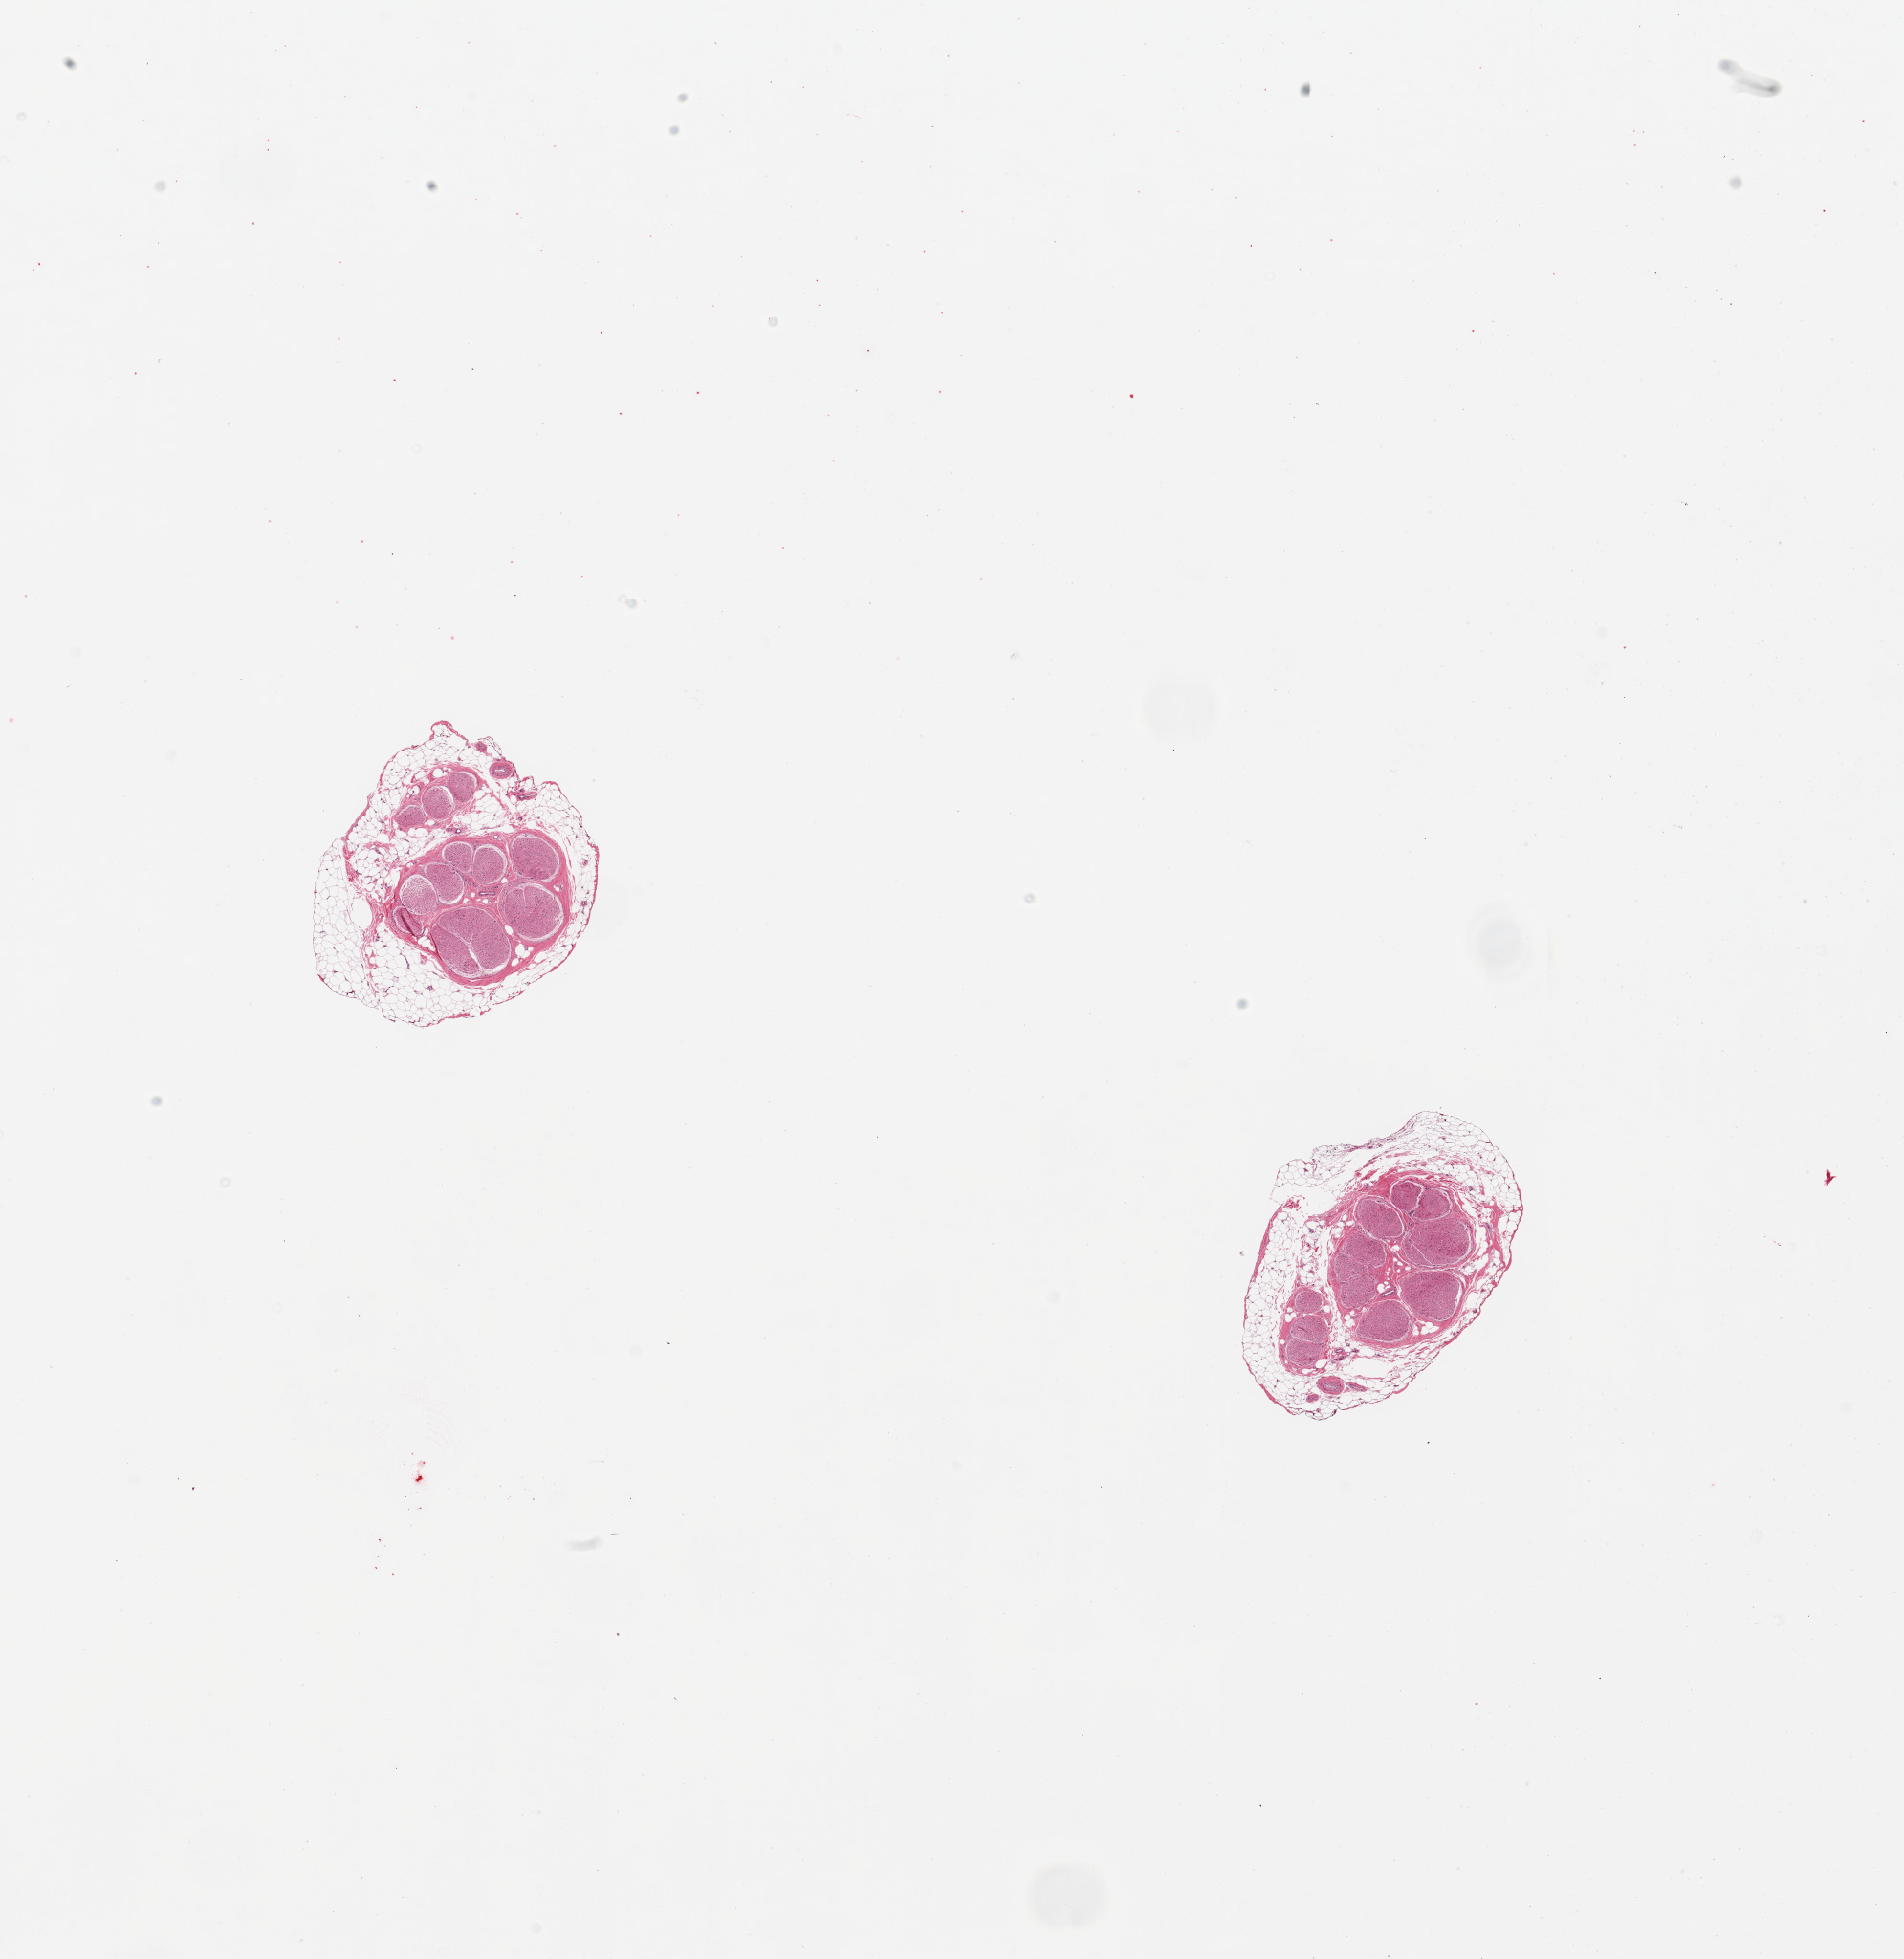
Whole-slide image, hematoxylin and eosin (H&E) stain — a low-resolution overview of the entire scanned area, about 15.8 x 16.2 mm; PAXgene-fixed paraffin-embedded (PFPE) section; target tissue: tibial nerve; donor tissue sample. Donor: female.
• reviewer comment on this tissue sample: 2 pieces; 50% & 40% external fat